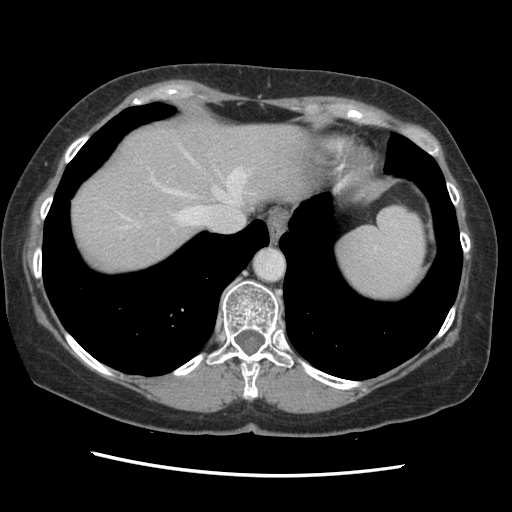
Contrast-enhanced abdominal CT, one axial slice. Slice 118 of 141 in the series (ordered by position). Soft-tissue window (W 400 / L 40 HU). 2.5 mm slice thickness. 512 × 512 image matrix, field of view 330 × 330 mm. Female patient, age 61 years. Case-level facts recorded for this patient, not image findings: diagnosis: colorectal cancer liver metastases, imaged before liver resection; multiple liver metastases: no; largest metastasis: 2.4 cm.
Annotated regions visible in this slice (outlined manually by an expert reader):
- hepatic veins: box from (x=120, y=147) to (x=248, y=227) px
- liver: (x=70, y=120)–(x=308, y=274)
- planned liver remnant (the part of the liver to remain after resection): (x=70, y=120)–(x=309, y=274)